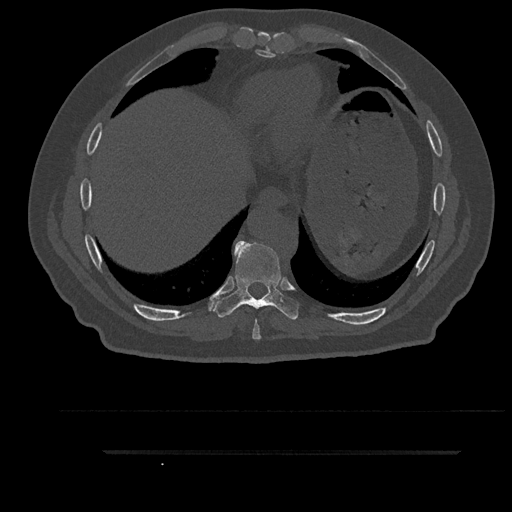
CT including the spine, one axial slice. Slice 435 of 797 in the series (ordered by position). Reconstruction kernel Br40s/3. Bone window (W 1800 / L 400 HU). 0.5 mm slice thickness. 512 × 512 image matrix. Patient: male, 63 years. Case-level facts recorded for this patient, not image findings: primary cancer: renal; vertebrae with lytic lesions (as recorded): T8.
Annotated regions visible in this slice (semi-automatic segmentation, software-assisted and operator-edited):
- T8 vertebra: bounding box (x1, y1, x2, y2) in pixels: (252, 320, 261, 340)
- T9 vertebra: (212, 241, 299, 320)